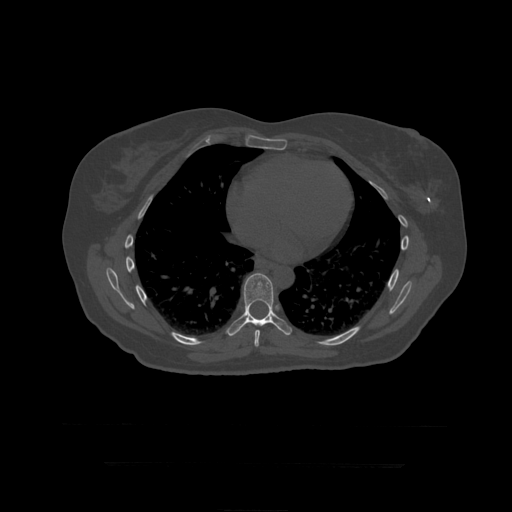
CT including the spine, one axial slice. Position 266 of 399 along the scan axis. 120 kVp. Bone window (W 1800 / L 400 HU). 1.25 mm slice thickness. 512 × 512 image matrix, field of view 450 × 450 mm. Patient age 41 years. Case-level facts recorded for this patient, not image findings: primary cancer: breast.
Annotated regions visible in this slice (semi-automatic segmentation, software-assisted and operator-edited):
- T8 vertebra: bounding box <254,330,260,347> (left, top, right, bottom; pixels)
- T9 vertebra: <226,273,292,336>